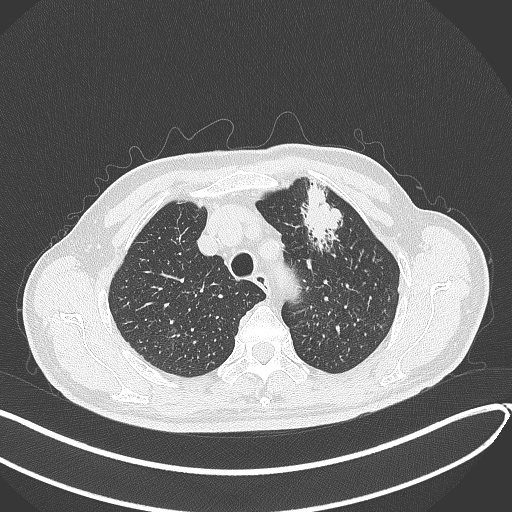
Chest CT, one axial slice; slice 340 of 459 in the series (ordered by position); reconstruction kernel B70f; 120 kVp; lung window (W 1500 / L -600 HU); 1 mm slice thickness; 512 × 512 image matrix. Patient: male, 74 years. Case-level facts recorded for this patient, not image findings: clinical TNM (as recorded): T2b N0 M1c.
Outlined on this slice (rectangle marked by the reading radiologist):
- lung tumour (recorded histology: adenocarcinoma): bounding box [x1, y1, x2, y2] px = [297, 175, 350, 257]